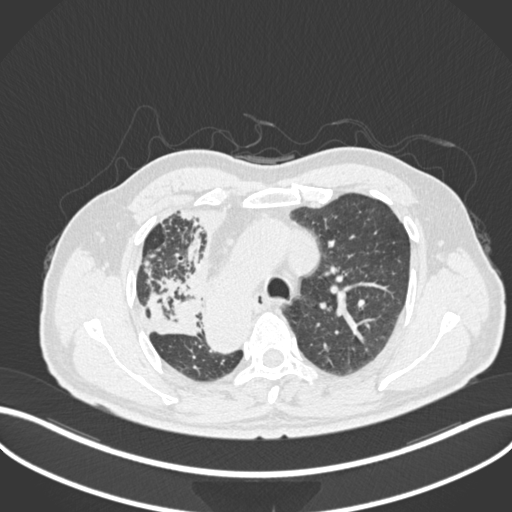
Chest CT, one axial slice. Slice 171 of 206 in the series (ordered by position). Lung window (W 1500 / L -600 HU). 512 × 512 image matrix, field of view 400 × 400 mm. Male patient, age 67 years. Case-level facts recorded for this patient, not image findings: clinical TNM (as recorded): T2a N0 M0.
Outlined on this slice (rectangle marked by the reading radiologist):
- lung tumour (recorded histology: squamous cell carcinoma): bounding box [x1, y1, x2, y2] px = [142, 283, 201, 337]